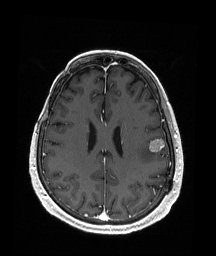
Brain MRI from a brain-tumour surgery series, one axial slice. T1-weighted post-contrast. 216 × 256 image matrix, field of view 211 × 250 mm. Case-level facts recorded for this patient, not image findings: histopathology: Metastatic Malignant Melanoma.
Structures marked on this image (manually delineated by an expert):
- tumour: box from (x=148, y=138) to (x=165, y=152) px